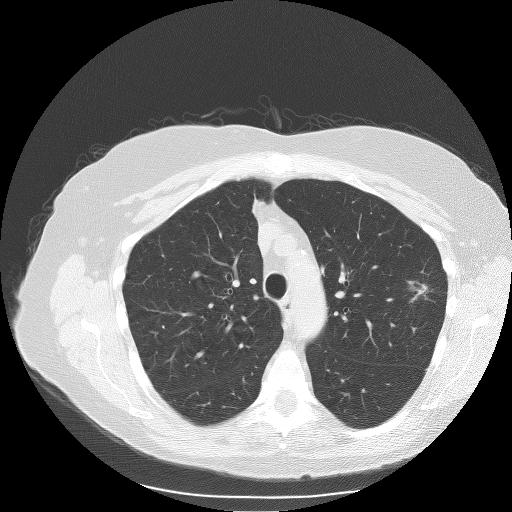
Chest CT (low-dose screening protocol), one axial image. Baseline annual screen. Lung window (W 1500 / L -600 HU). Lung (sharp) reconstruction kernel (BONE). 512 × 512 image matrix. Female participant, aged 71 years at enrolment. Former smoker at enrolment.
Expert-annotated lung lesion, box from (x=399, y=274) to (x=445, y=314) px. The exam's reader record, not a measurement of the box and not confirmed to be the same lesion: non-calcified nodule or mass ≥4 mm, left upper lobe, 15 × 9 mm, spiculated (stellate) margins, soft tissue attenuation. Lung cancer was diagnosed 77 days after this screen: adenocarcinoma, NOS, left upper lobe, moderately differentiated (G2), stage IA (AJCC 6th edition), 15 mm at pathology.